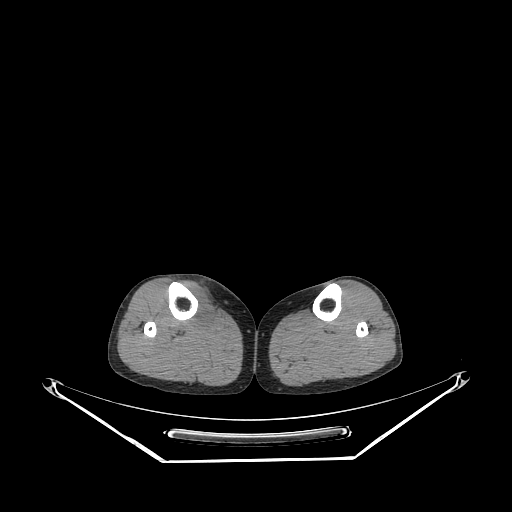
CT of an extremity soft-tissue mass (from a PET/CT study), one axial slice; slice 143 of 267 in the series (ordered by position); reconstruction kernel STANDARD; 140 kVp; soft-tissue window (W 400 / L 40 HU); 3.75 mm slice thickness; 512 × 512 image matrix. Female patient. From the clinical record (not read from this slice): histological type: undifferentiated – high grade; grade: high; site of the primary tumour: right thigh.
Annotated regions visible in this slice (expert contour drawn on MRI and transferred to this co-registered scan by the dataset authors):
- gross tumour volume (mass): bounding box (x1, y1, x2, y2) in pixels: (181, 281, 213, 327)